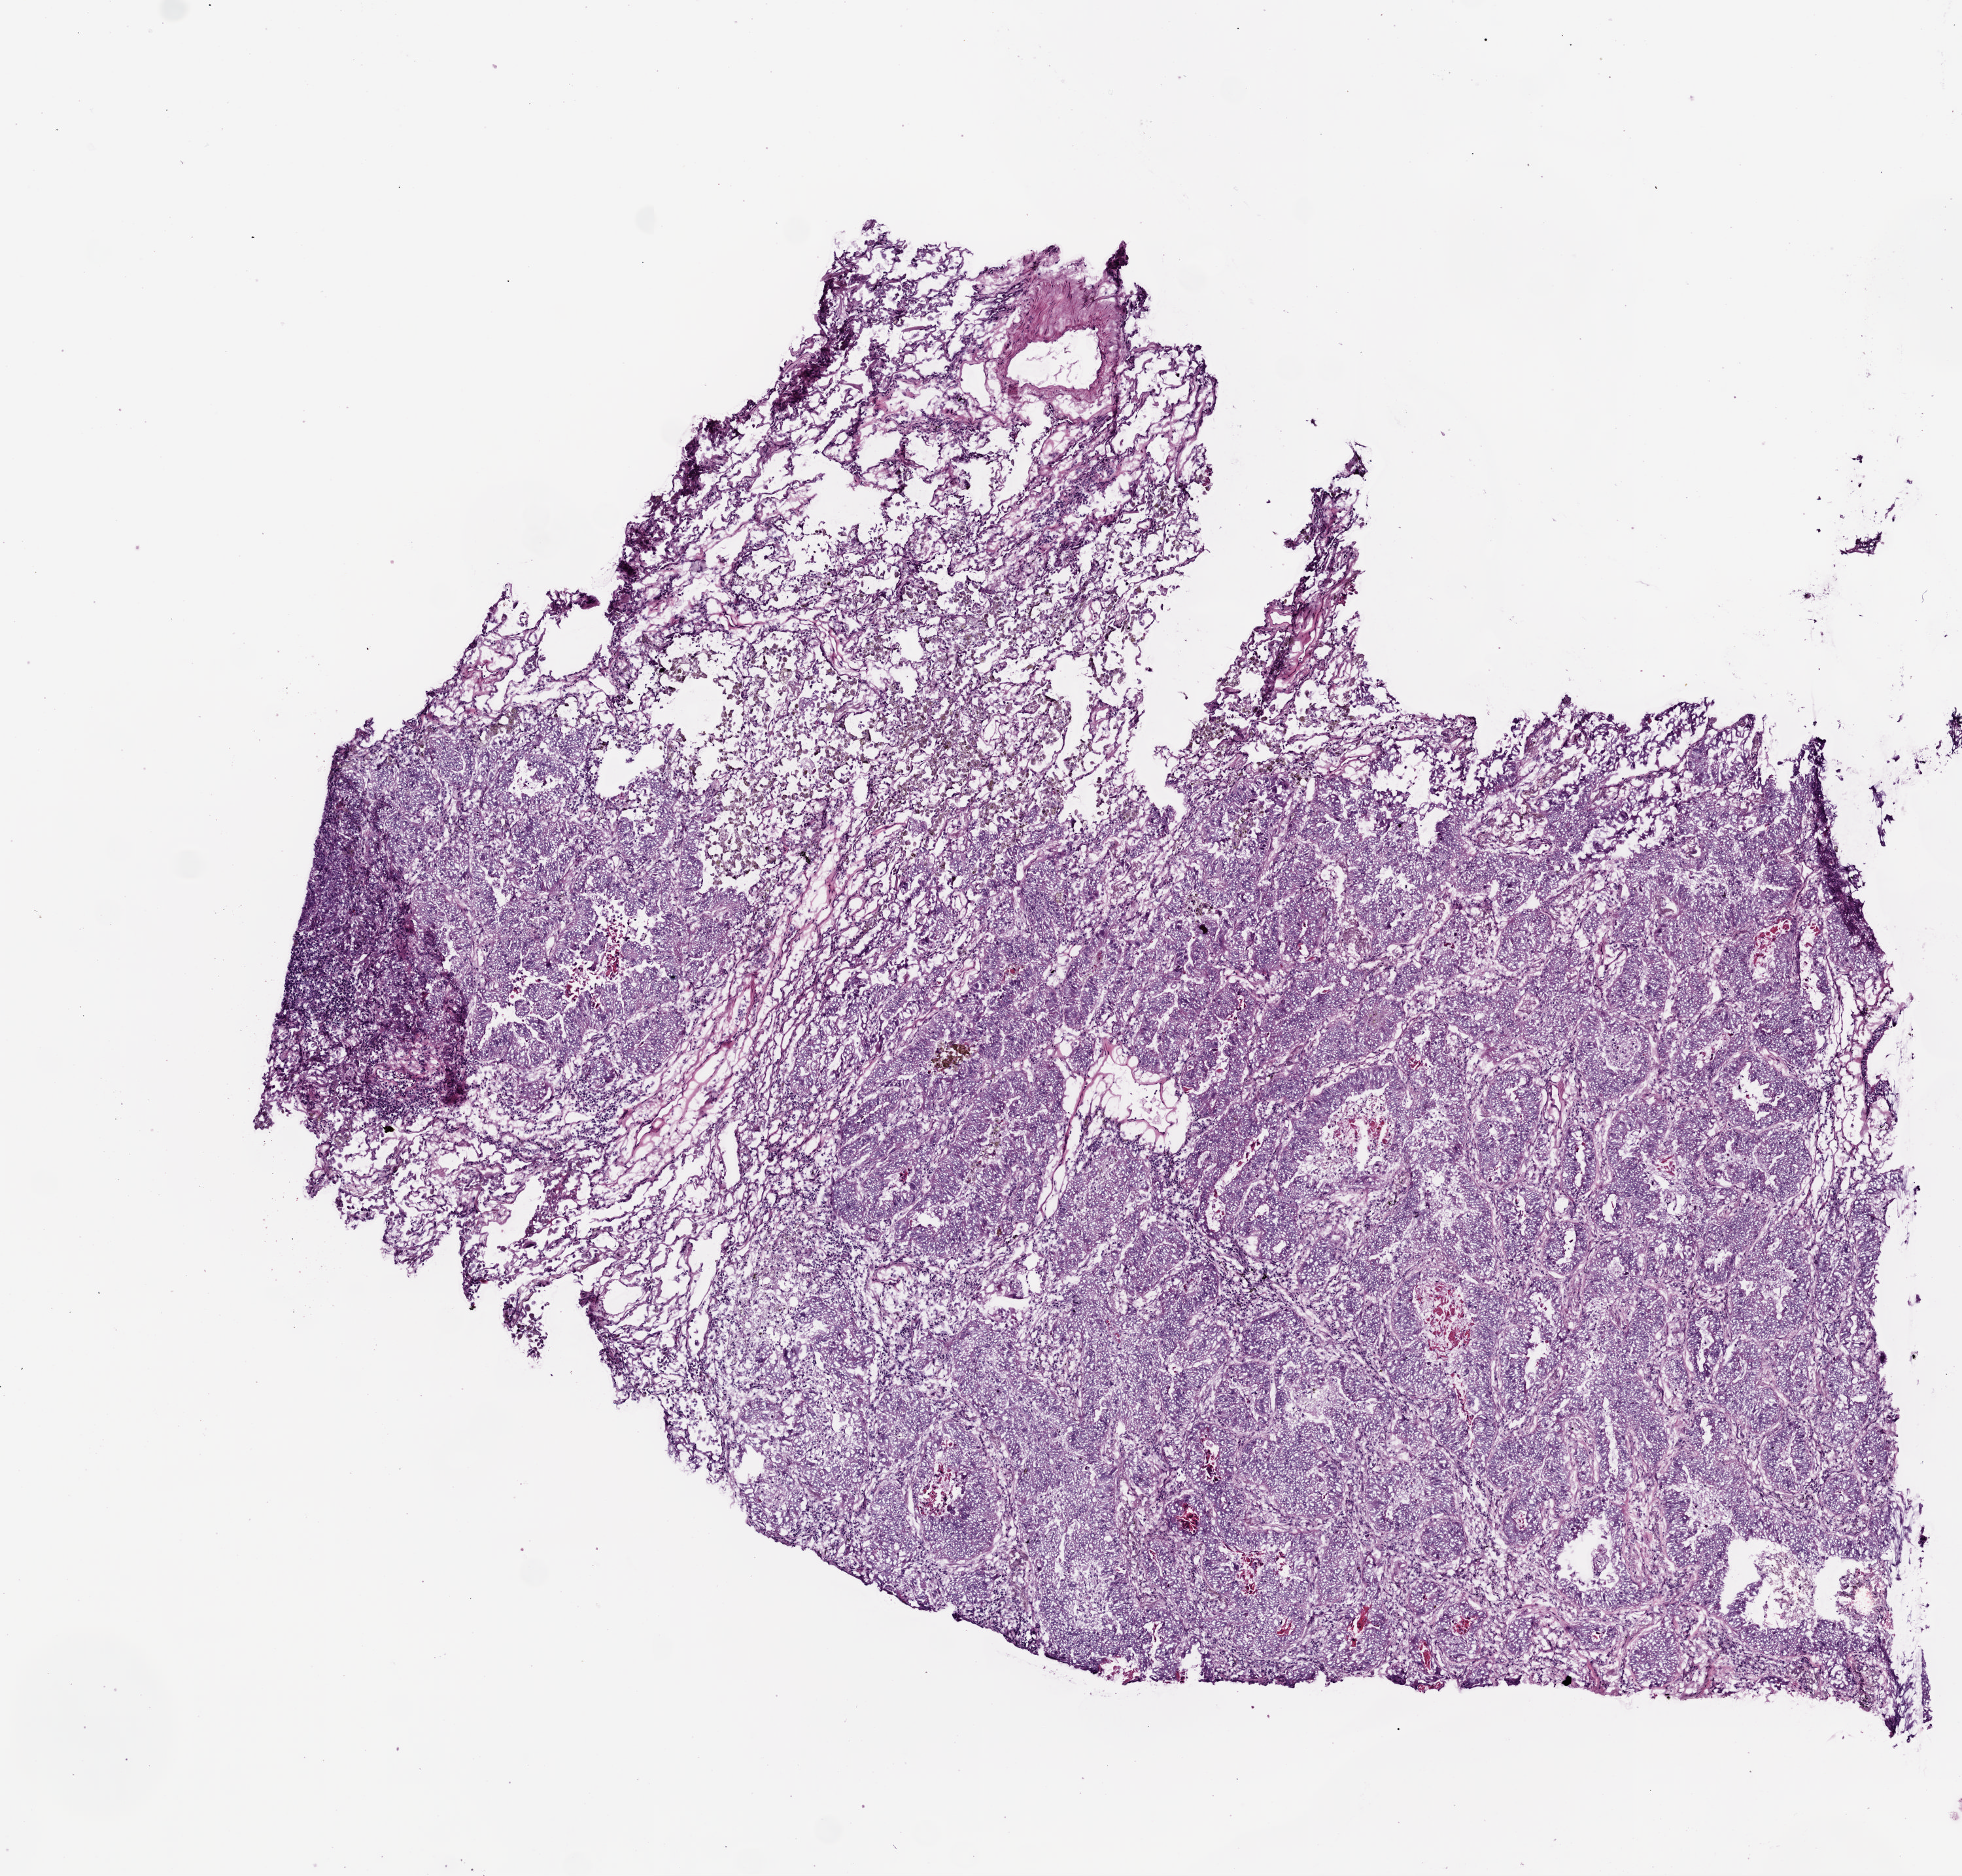
Hematoxylin and eosin (H&E) stained whole-slide image, a low-resolution overview of the entire scanned area, about 6.0 x 5.8 mm (from a 20x scan); frozen section from the bottom of the tissue portion; lung, primary tumour sample. Male, age 70 years at initial diagnosis. Pathologist review of this section (percent, as recorded): tumour cells 67%, tumour nuclei 75%, normal cells 25%, stromal cells 5%, necrosis 3%.
• pathologic diagnosis: Adenocarcinoma with mixed subtypes (upper lobe, lung)
• AJCC pathologic stage: IIB